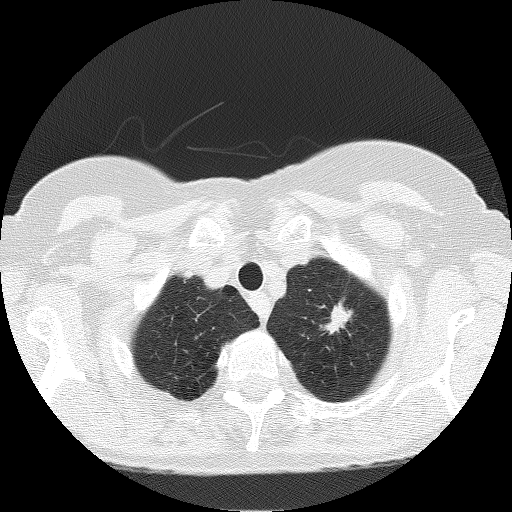
Axial slice from a low-dose chest CT screening exam. Baseline screening round. Lung window (W 1500 / L -600 HU). 2 mm slice thickness. 120 kVp. Slice 16 of 166 in the series. Female, age 66 years at enrolment. Current smoker at enrolment.
Expert-annotated lung lesion, bounding box (x1, y1, x2, y2) in pixels: (312, 286, 370, 348). The screening reader recorded 3 non-calcified nodules or masses ≥4 mm on this exam (left upper lobe, left upper lobe, left upper lobe); which of them this box marks is not recorded. Later outcome: lung cancer diagnosed 156 days after this screen — adenocarcinoma, NOS, left upper lobe, moderately differentiated (G2), stage IB (AJCC 6th edition), 17 mm at pathology.